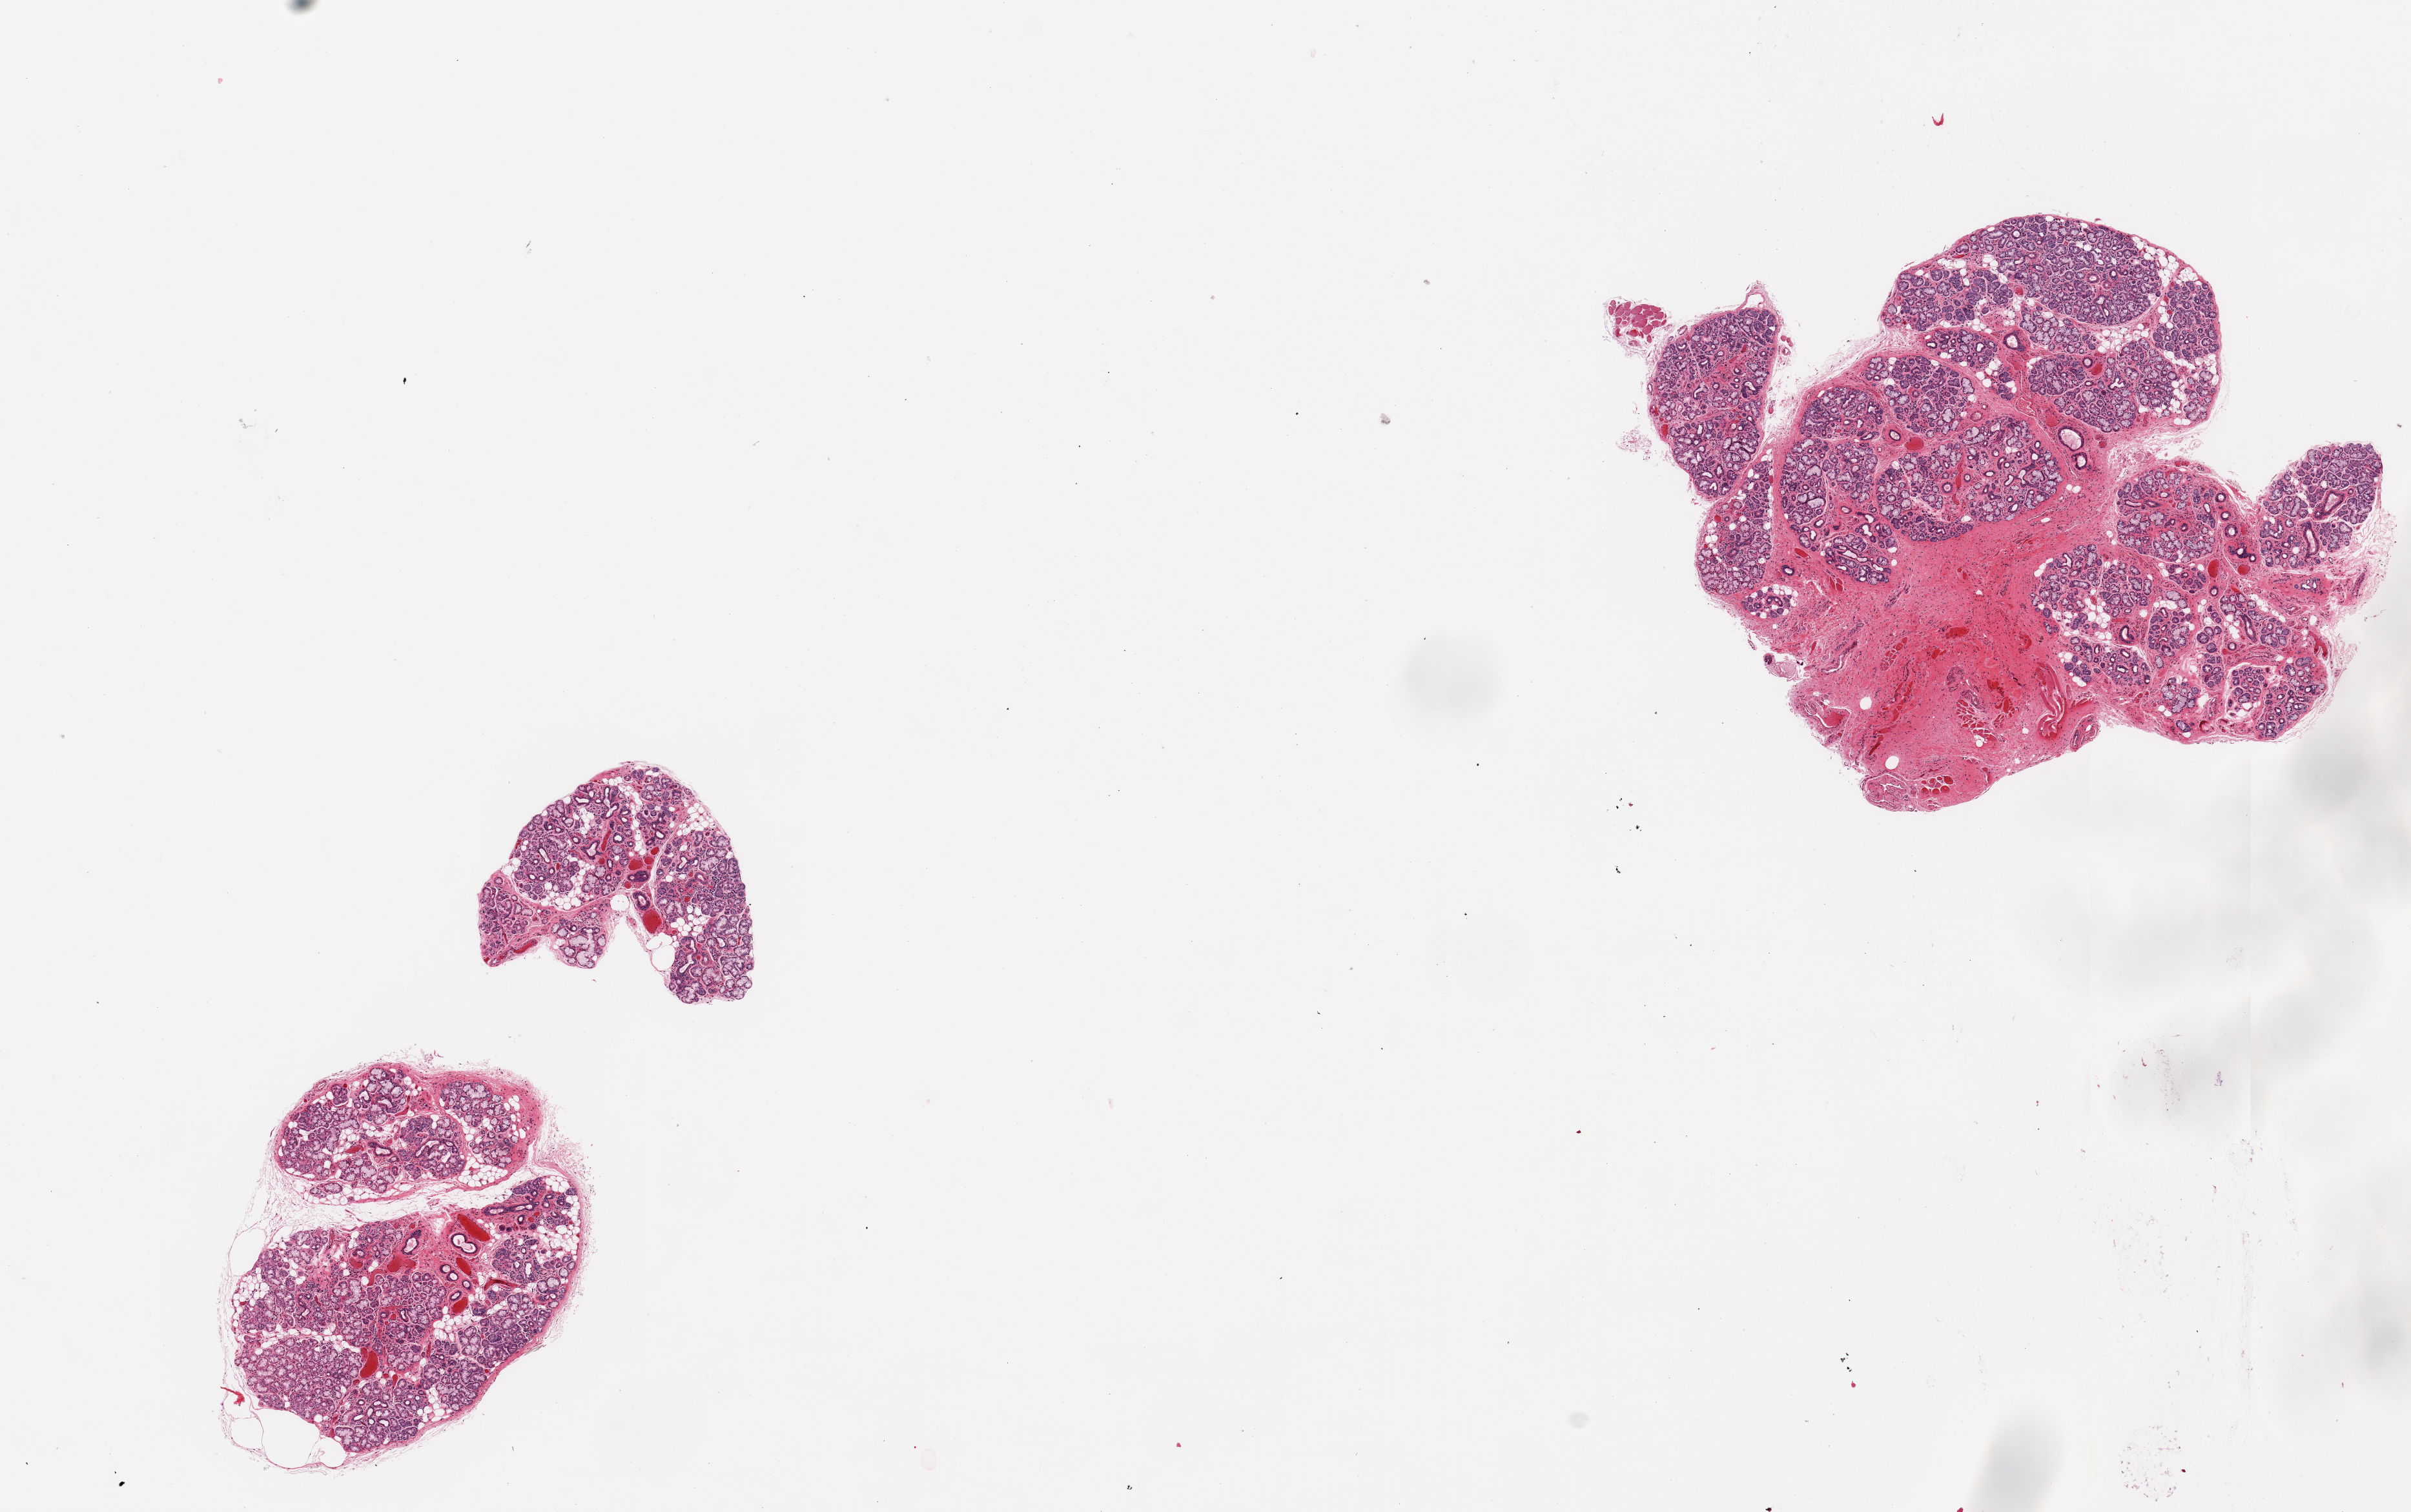
Digitized hematoxylin and eosin (H&E)-stained section — shown as a low-resolution overview of the whole scanned area (about 14.8 x 9.3 mm), PAXgene-fixed, paraffin-embedded tissue, sampled site (target tissue): minor salivary gland, donor tissue sample. Donor sex: male.
Reviewer comment on this tissue sample: 3 pieces; predominantly salivary gland elements, 1 piece includes ~25% fibrous stroma/skeletal muscle.